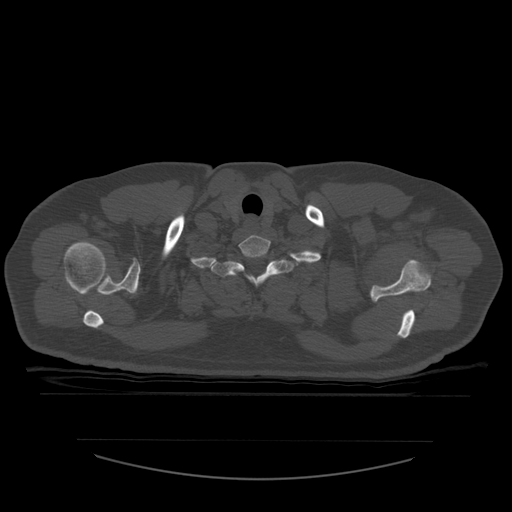
CT including the spine, one axial slice; slice 472 of 532 in the series (ordered by position); reconstruction kernel STANDARD; 120 kVp; bone window (W 1800 / L 400 HU); 512 × 512 image matrix, field of view 441 × 441 mm. Patient age 44 years. Case-level facts recorded for this patient, not image findings: primary cancer: soft tissue sarcoma.
Annotated regions visible in this slice (semi-automatically segmented with operator editing):
- T1 vertebra: box from (x=211, y=255) to (x=301, y=287) px